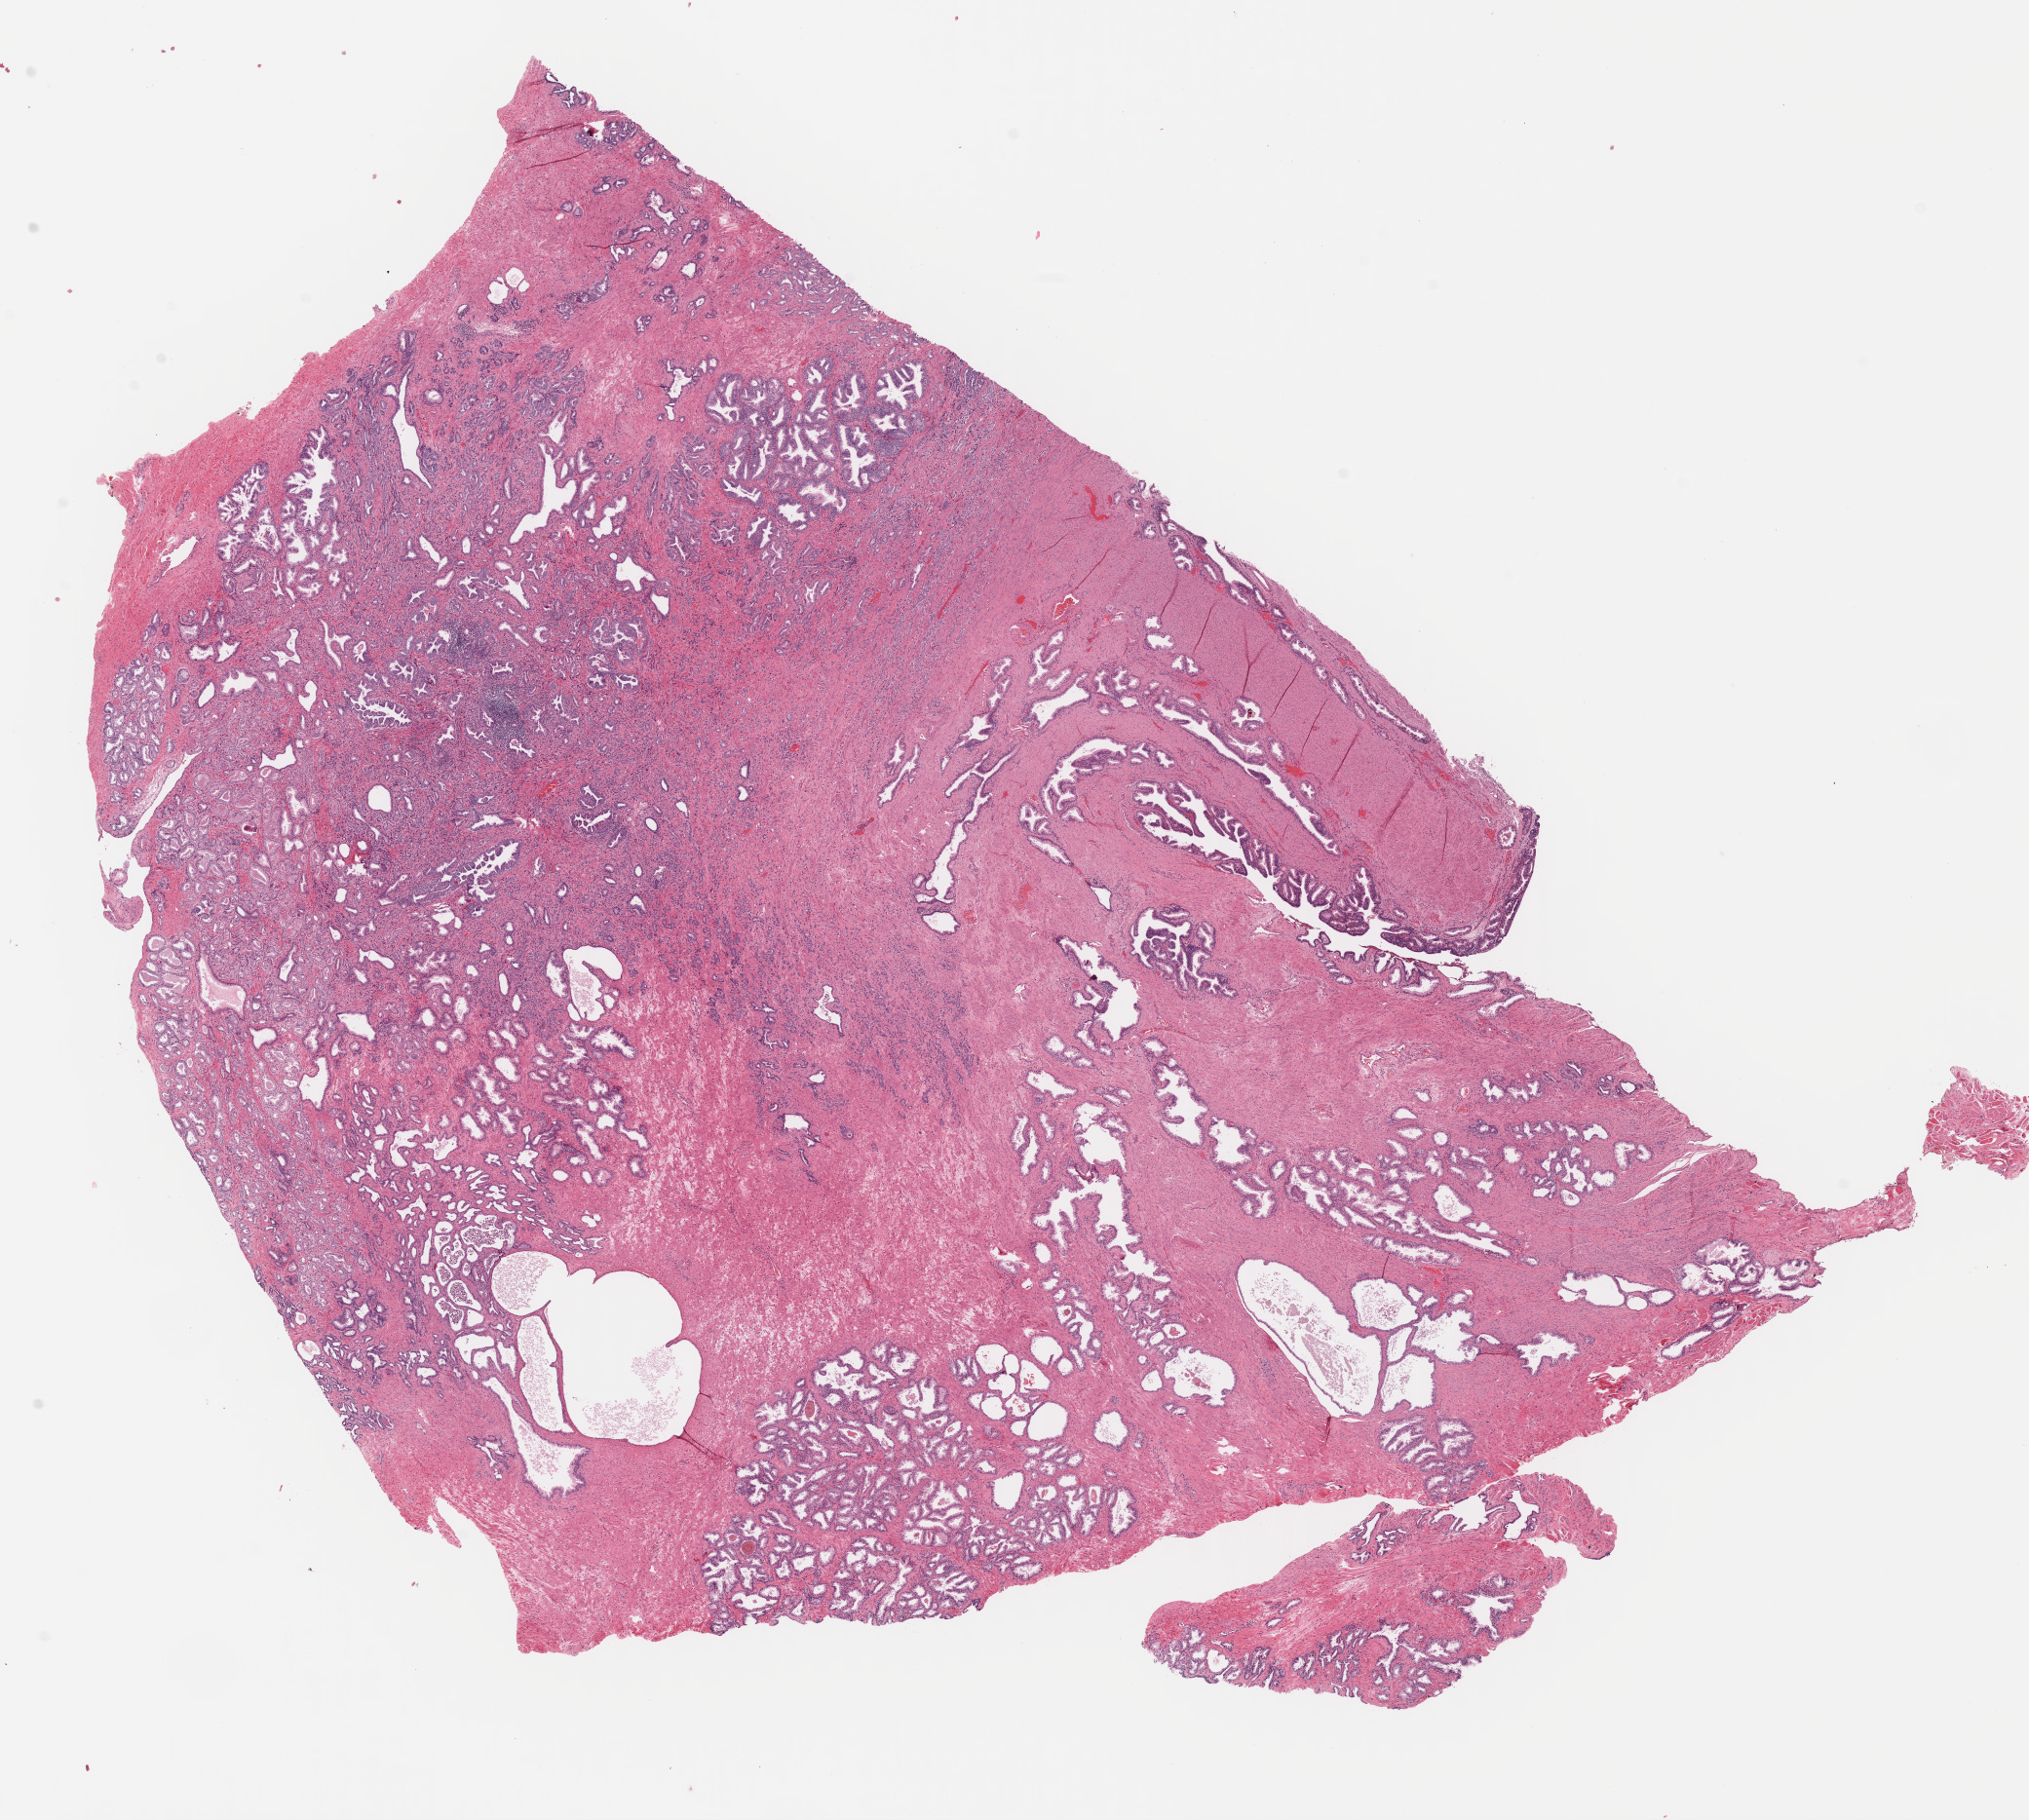
H&E-stained whole-slide image, a low-resolution overview of the entire scanned area, about 16.4 x 14.7 mm (acquisition: 40x scan); formalin-fixed paraffin-embedded (FFPE) diagnostic section; primary tumour sample from the prostate. Male patient; age at initial diagnosis 53 years. Gleason score: 8 (3+5).
Diagnosis: Adenocarcinoma, NOS (prostate gland).